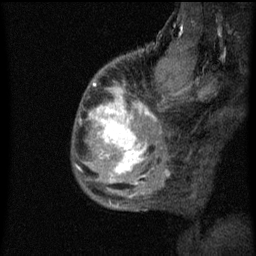
Breast MRI (dynamic contrast-enhanced), one sagittal slice; slice 16 of 60 in the series (ordered by position); dynamic contrast-enhanced series, image 2 of 3 at this slice position (ordered by acquisition); 1.5 T; TE 4.2 ms, TR 8 ms; 2 mm slice thickness; 256 × 256 image matrix, field of view 180 × 180 mm. Female patient, age 50 years.
Outlined on this slice (semi-automatically segmented with operator editing):
- analysis volume of interest (the breast-tissue region the enhancement analysis was run in; not a lesion): bounding box <72,64,141,187> (left, top, right, bottom; pixels)
- tumour enhancement mask (voxels above the 70 % enhancement threshold inside the analysis volume of interest): <90,94,141,173>